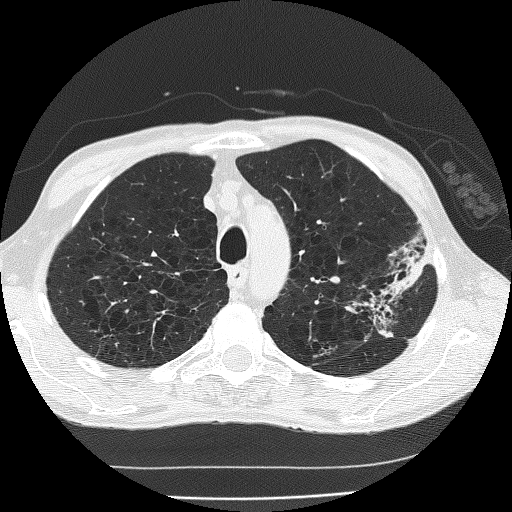
Low-dose screening chest CT, one axial slice; slice 144 of 185 in the series (ordered by position); 120 kVp; lung window (W 1500 / L -600 HU); 2 mm slice thickness; 512 × 512 image matrix.
Outlined on this slice (expert manual segmentation):
- lesion 1 (tumor, upper lobe of left lung): bounding box [x1, y1, x2, y2] px = [385, 253, 425, 298]